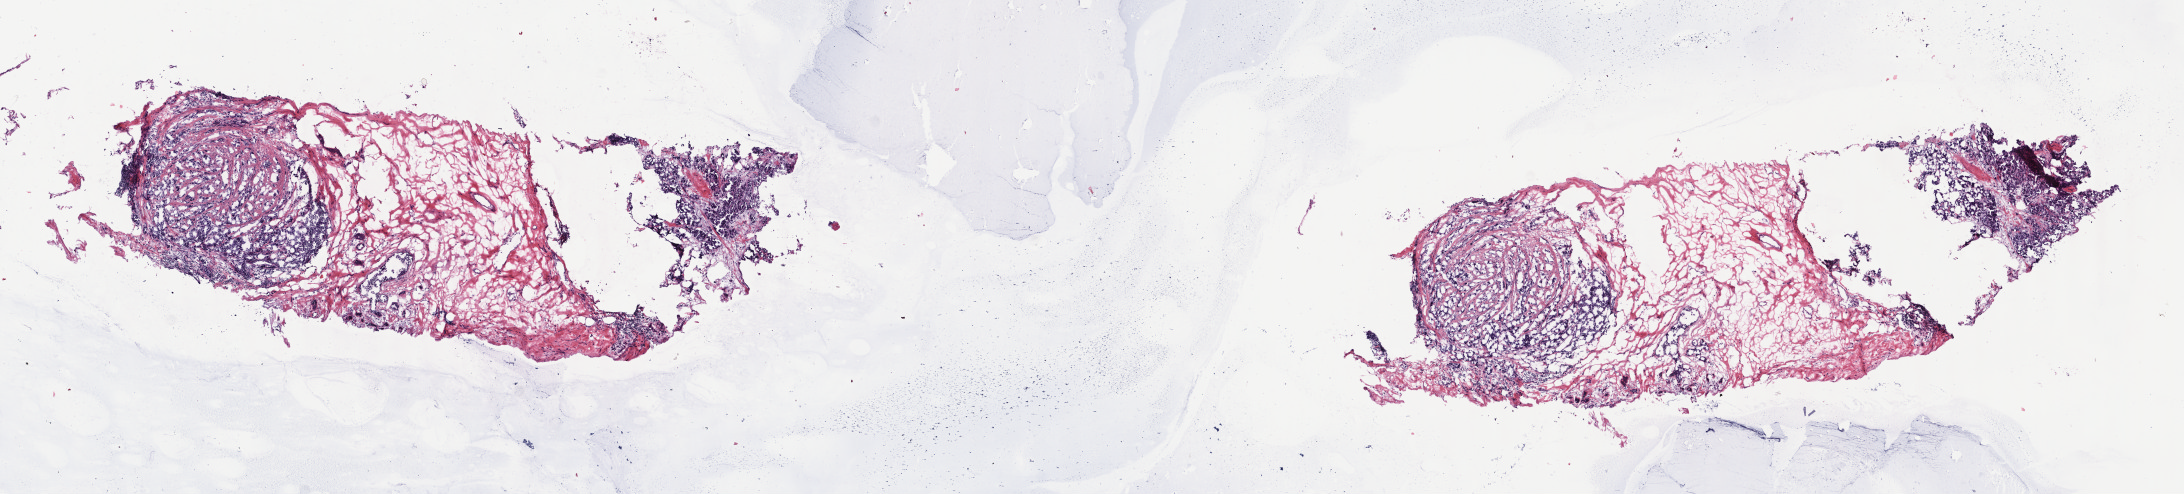
Digitized H&E-stained tissue section (whole slide) — whole scanned area (about 17.4 x 3.9 mm, from a 40x scan) shown as a low-resolution overview; frozen section; breast, primary tumour sample. Female patient; age at initial diagnosis 42 years. Pathologist review of this section (percent, as recorded): tumour cells 50%, tumour nuclei 65%, normal cells 50%, stromal cells 0%, necrosis 0%. Infiltration values recorded for this section: lymphocyte infiltration 20%, monocyte infiltration 0%, neutrophil infiltration 0%.
Lymph nodes positive (case pathology): 2 of 12 examined. AJCC pathologic stage: IIB (6th edition). TNM: T2 N1a M0. Laterality: left. Pathologic diagnosis: Infiltrating duct carcinoma, NOS.